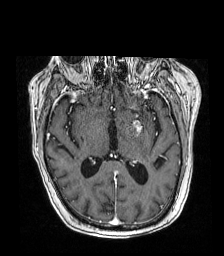
Brain MRI from a brain-tumour surgery series, one axial slice. Slice 91 of 192 in the series (ordered by position). T1-weighted post-contrast. 1 mm slice thickness. 224 × 256 image matrix, field of view 219 × 250 mm. Case-level facts recorded for this patient, not image findings: histopathology: Metastatic carcinoma from lung primary; tumour location: Left Frontal Caudate.
Structures marked on this image (expert manual segmentation):
- tumour: bounding box [x1, y1, x2, y2] px = [134, 116, 147, 133]